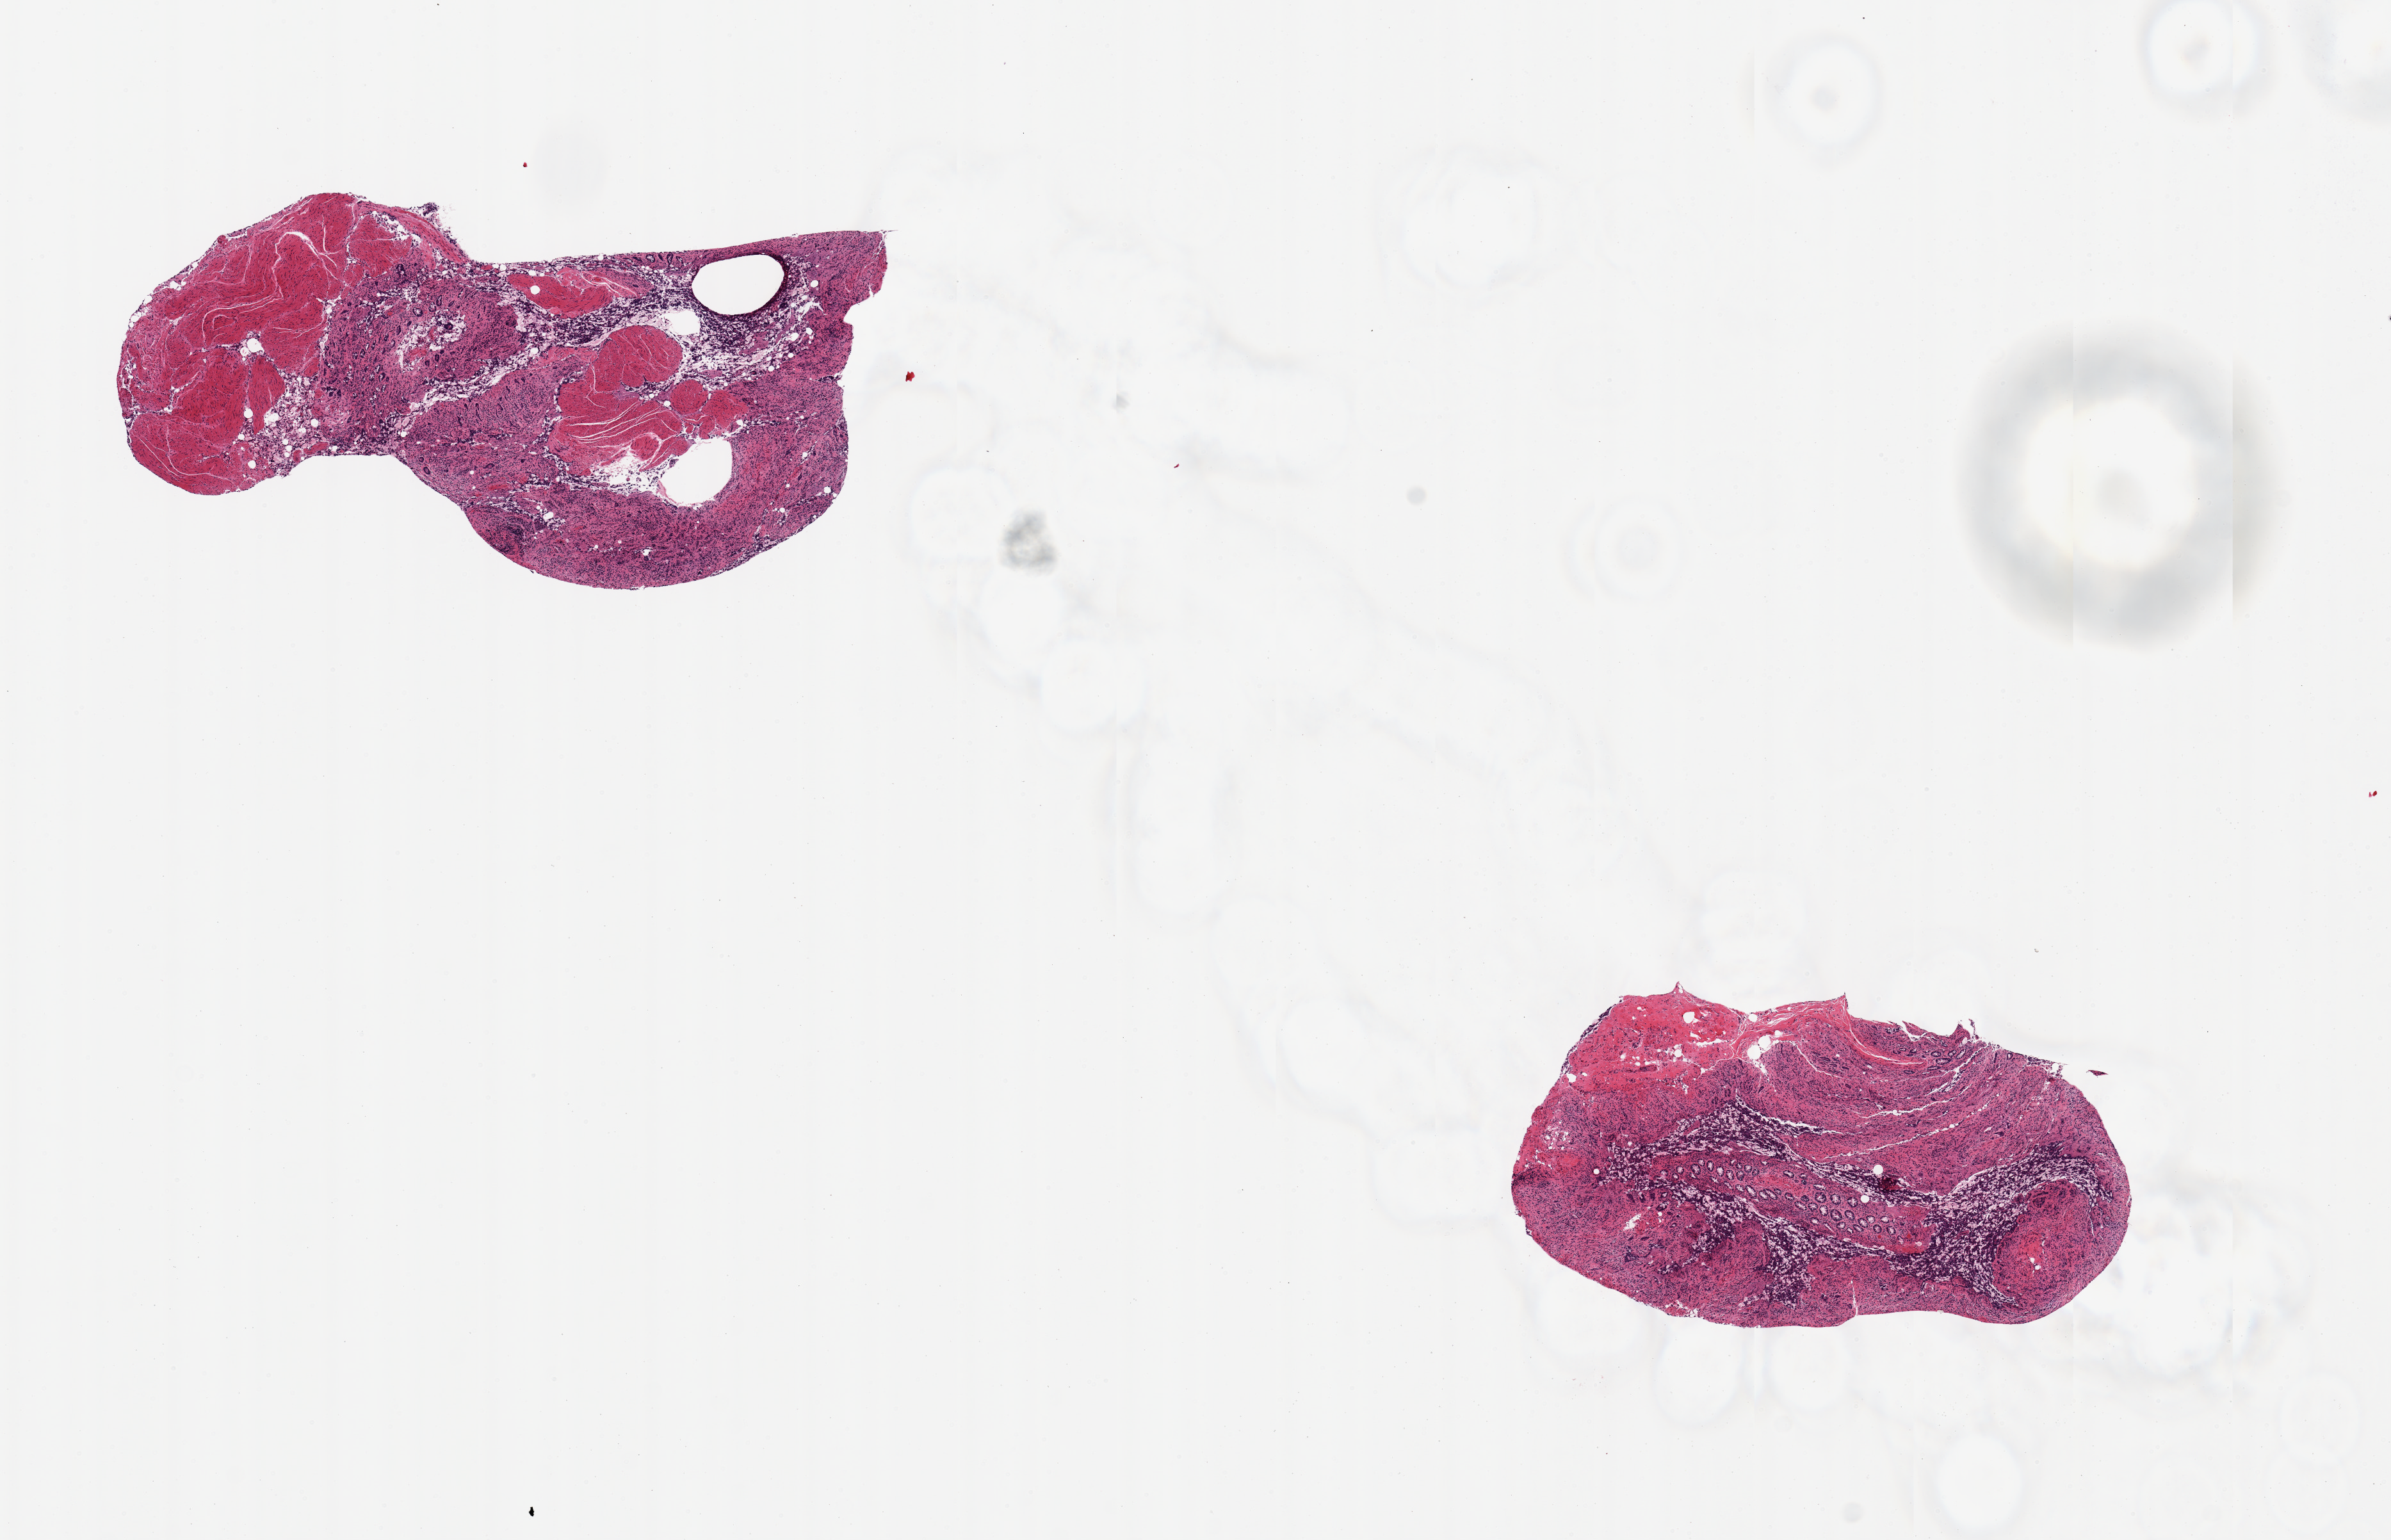
Whole-slide image, H&E stain — low-resolution overview of the scanned area, about 14.8 x 9.5 mm, PAXgene-fixed, paraffin-embedded tissue, target tissue: ileum, donor tissue sample. Donor: male.
Reviewer comment on this tissue sample: 2 pieces; moderate to severe autolysis of mucosa, no lymphoid nodules, muscularis also present (not target).